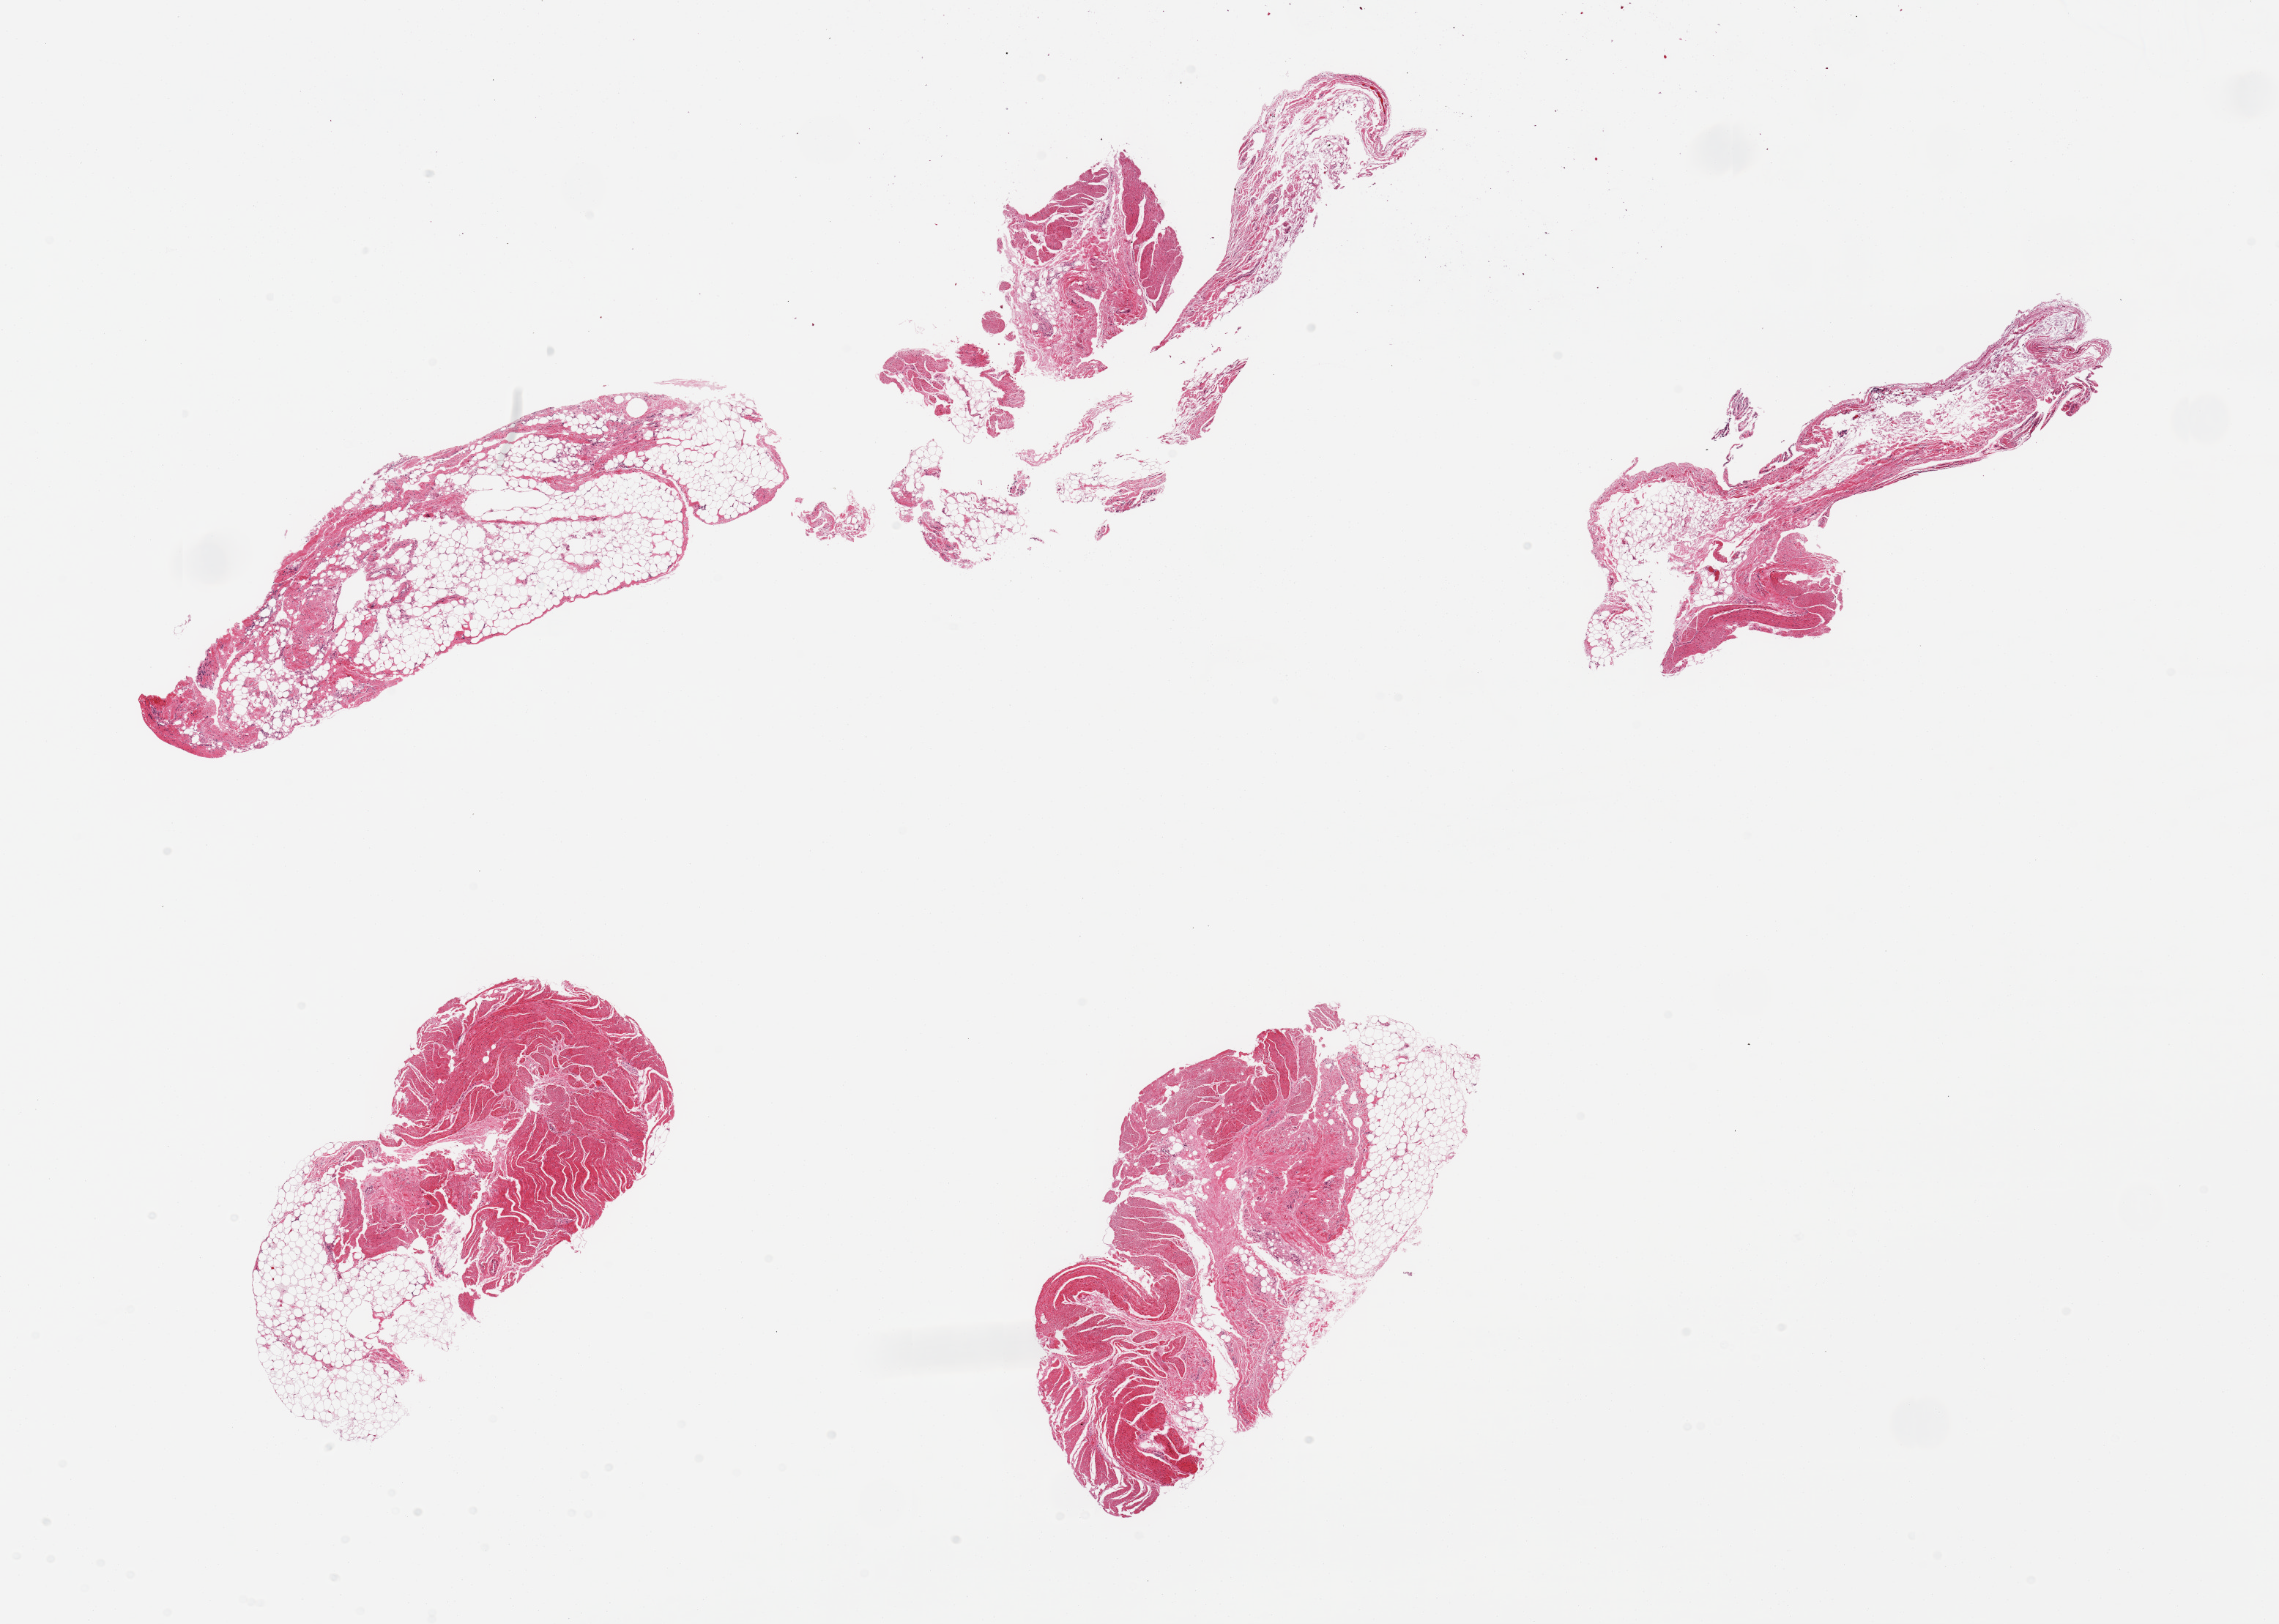
Haematoxylin and eosin whole-slide image, low-resolution overview of the scanned area, about 24.6 x 17.5 mm (from a 20x scan). PAXgene-fixed paraffin-embedded (PFPE) section. Target tissue: sigmoid colon. Donor tissue sample. Male donor.
- review note (as recorded): 5 pieces, ~40% target muscularis, rest is fat/fibrous tissue